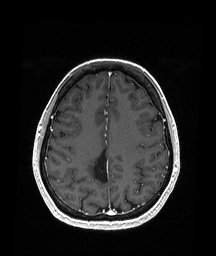
Brain MRI from a brain-tumour surgery series, one axial slice; position 68 of 151 along the scan axis; T1-weighted post-contrast; 1.05 mm slice thickness; 216 × 256 image matrix, field of view 211 × 250 mm. From the clinical record (not read from this slice): histopathology: Oligodendroglioma; WHO grade: 2; IDH mutation: yes.
Outlined on this slice (outlined manually by an expert reader):
- previous resection cavity: bounding box (x1, y1, x2, y2) in pixels: (94, 149, 109, 183)